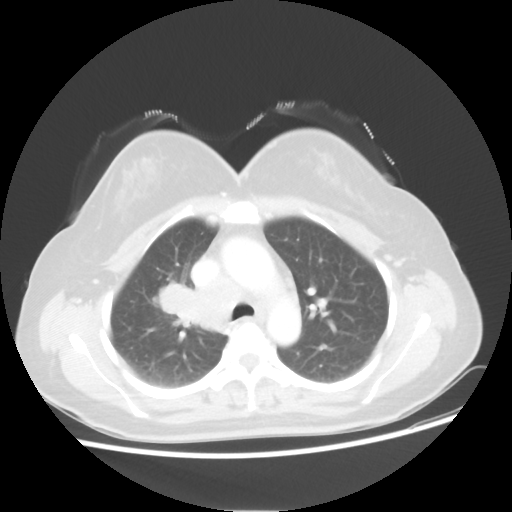
Chest CT, one axial slice. Slice 35 of 50 in the series (ordered by position). Lung window (W 1500 / L -600 HU). 5 mm slice thickness. 512 × 512 image matrix, field of view 360 × 360 mm. Patient: female, 40 years. From the clinical record (not read from this slice): clinical TNM (as recorded): T1c N3 M0; histopathological grade: G3.
Structures marked on this image (rectangle marked by the reading radiologist):
- lung tumour (recorded histology: small cell carcinoma): box from (x=157, y=284) to (x=192, y=327) px